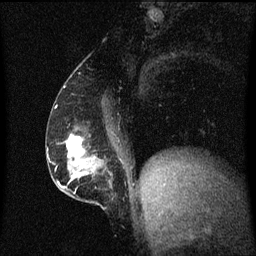
Breast MRI (dynamic contrast-enhanced), one sagittal slice; position 26 of 60 along the scan axis; dynamic contrast-enhanced series, image 2 of 3 at this slice position (ordered by acquisition); 1.5 T; TE 4.2 ms, TR 8.4 ms; 2 mm slice thickness; 256 × 256 image matrix. Female patient, age 52 years. From the clinical record (not read from this slice): setting: breast cancer imaged before/during neoadjuvant chemotherapy; receptor status: HER2-positive.
Annotated regions visible in this slice (semi-automatically segmented with operator editing):
- analysis volume of interest (the breast-tissue region the enhancement analysis was run in; not a lesion): bounding box (x1, y1, x2, y2) in pixels: (62, 132, 122, 203)
- tumour enhancement mask (voxels above the 70 % enhancement threshold inside the analysis volume of interest): (67, 136, 83, 159)